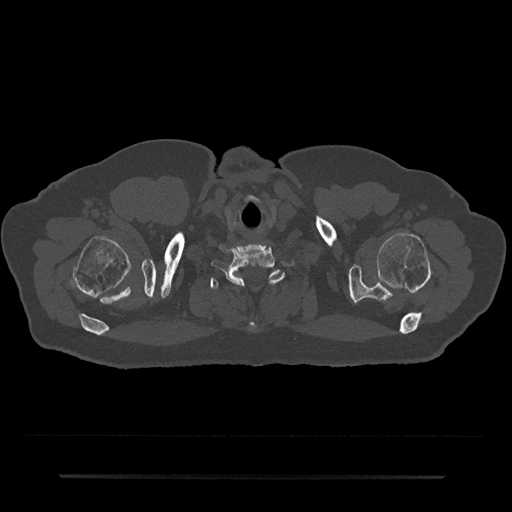
CT including the spine, one axial slice; slice 663 of 797 in the series (ordered by position); reconstruction kernel Br40s/3; bone window (W 1800 / L 400 HU); 512 × 512 image matrix, field of view 437 × 437 mm. Patient: male, 69 years. Case-level facts recorded for this patient, not image findings: primary cancer: prostate.
Outlined on this slice (semi-automatic segmentation, software-assisted and operator-edited):
- T1 vertebra: bounding box (x1, y1, x2, y2) in pixels: (210, 269, 282, 329)